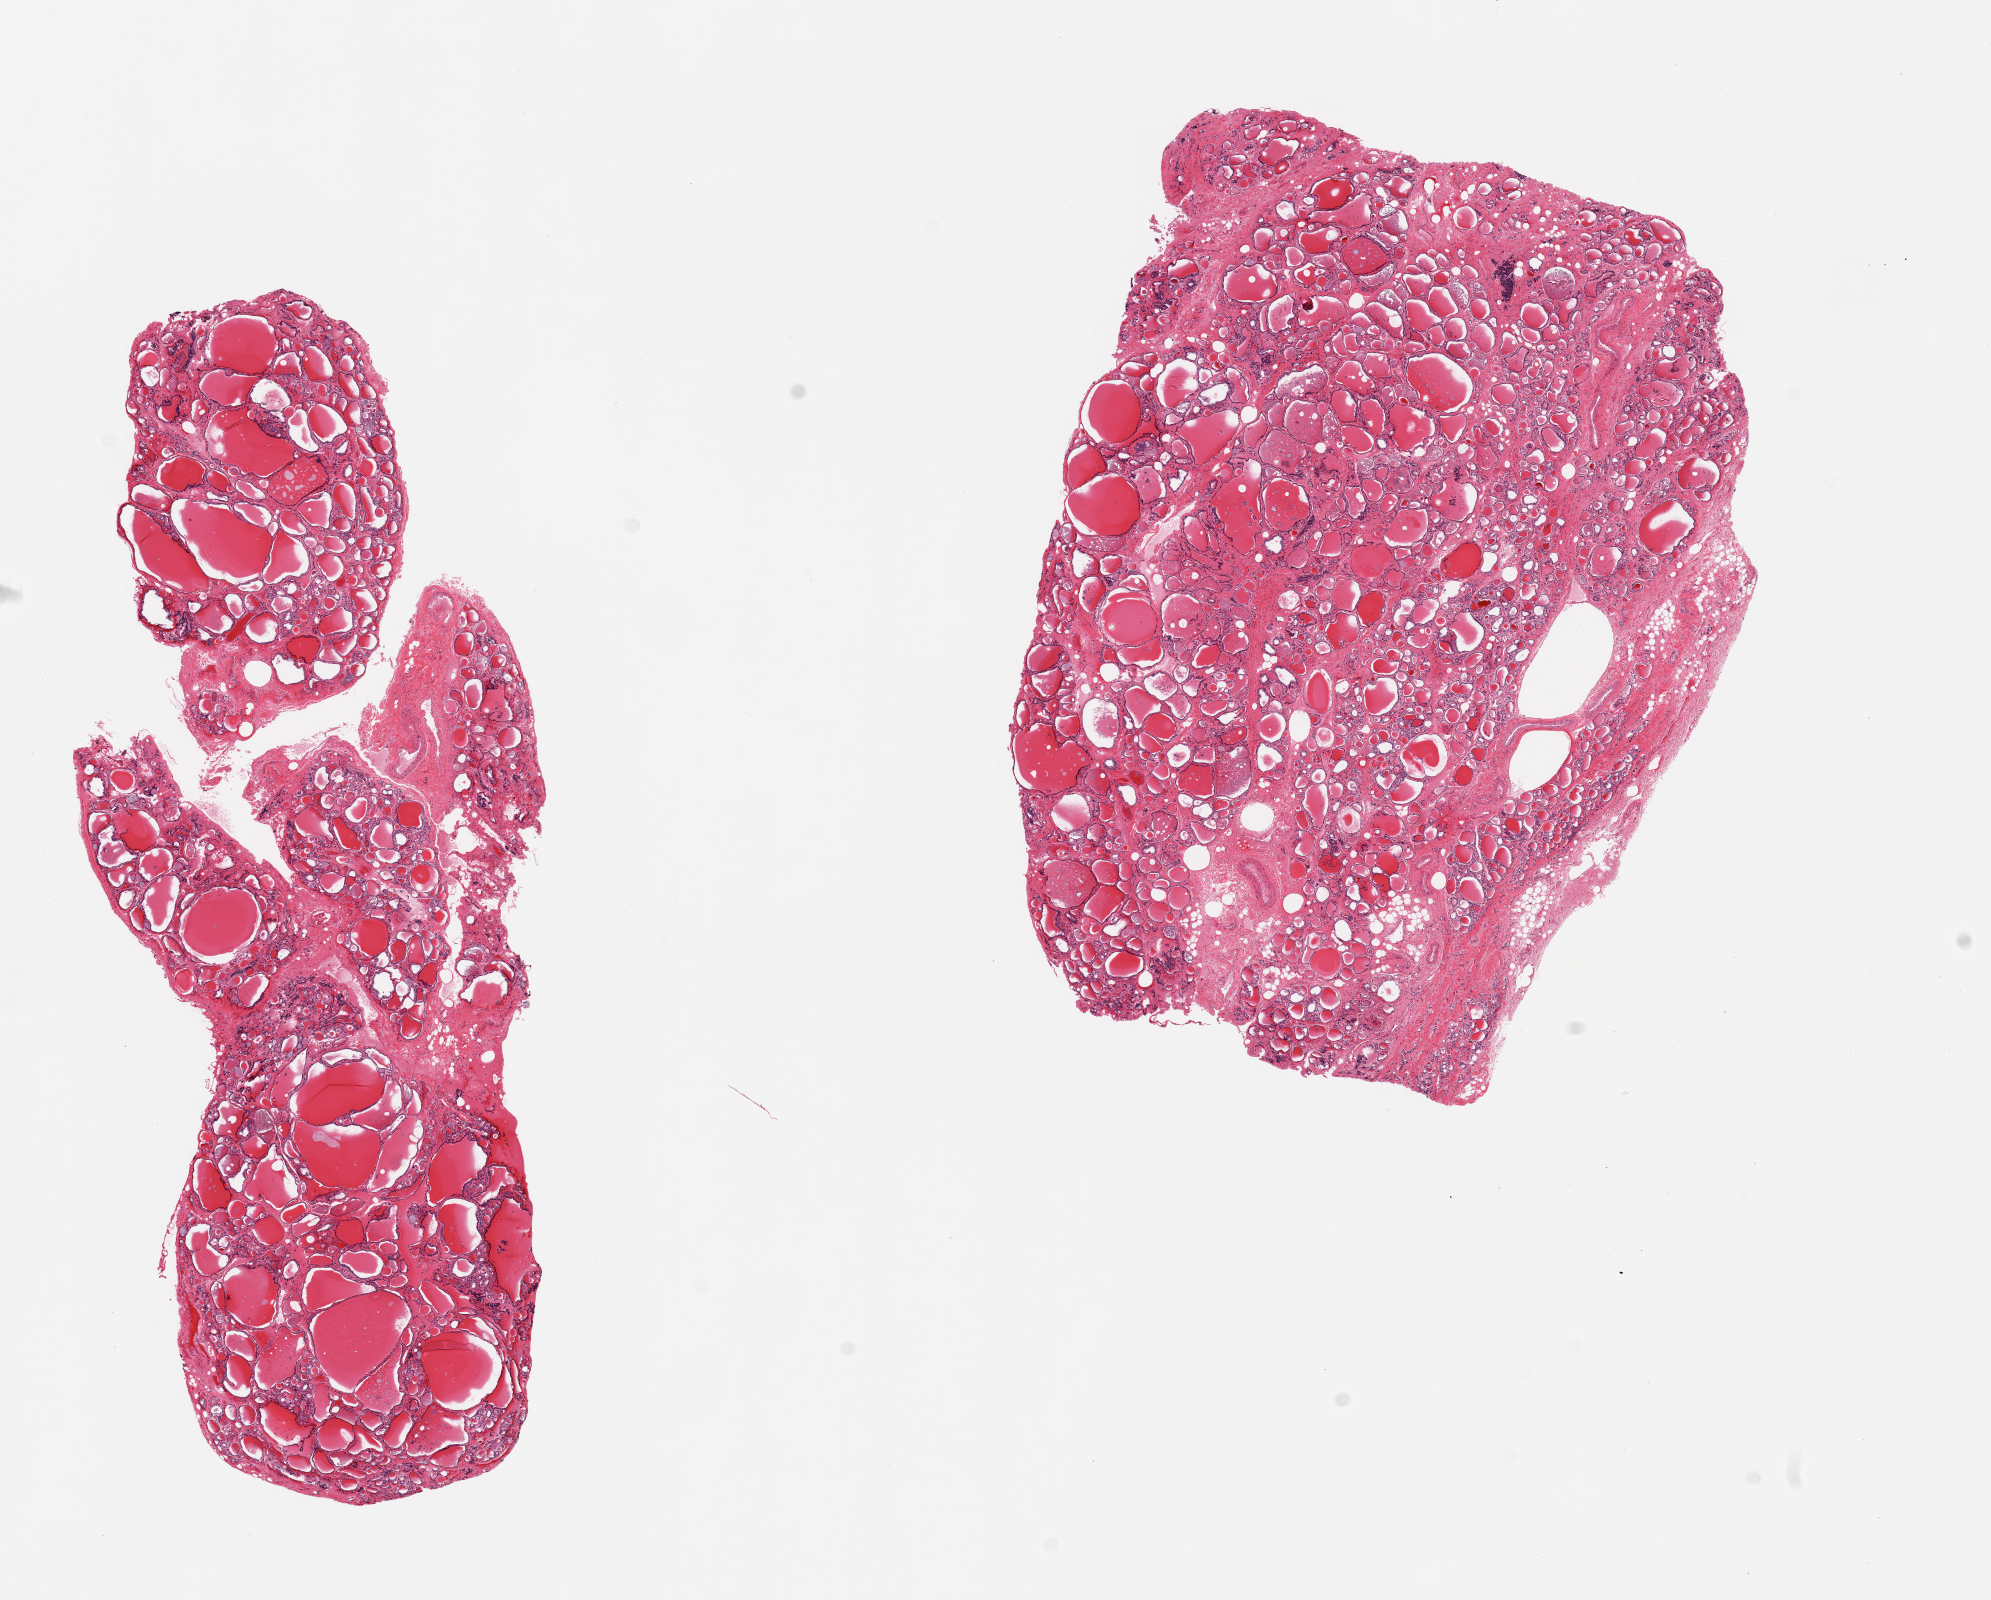
Digitized hematoxylin and eosin (H&E)-stained section, brightfield, low-resolution overview of the scanned area, about 15.8 x 12.7 mm. PAXgene-fixed paraffin-embedded (PFPE) section. Target tissue: thyroid. Donor tissue sample. Male donor.
Review note (as recorded): 2 pieces; some nodularity and regressive change.